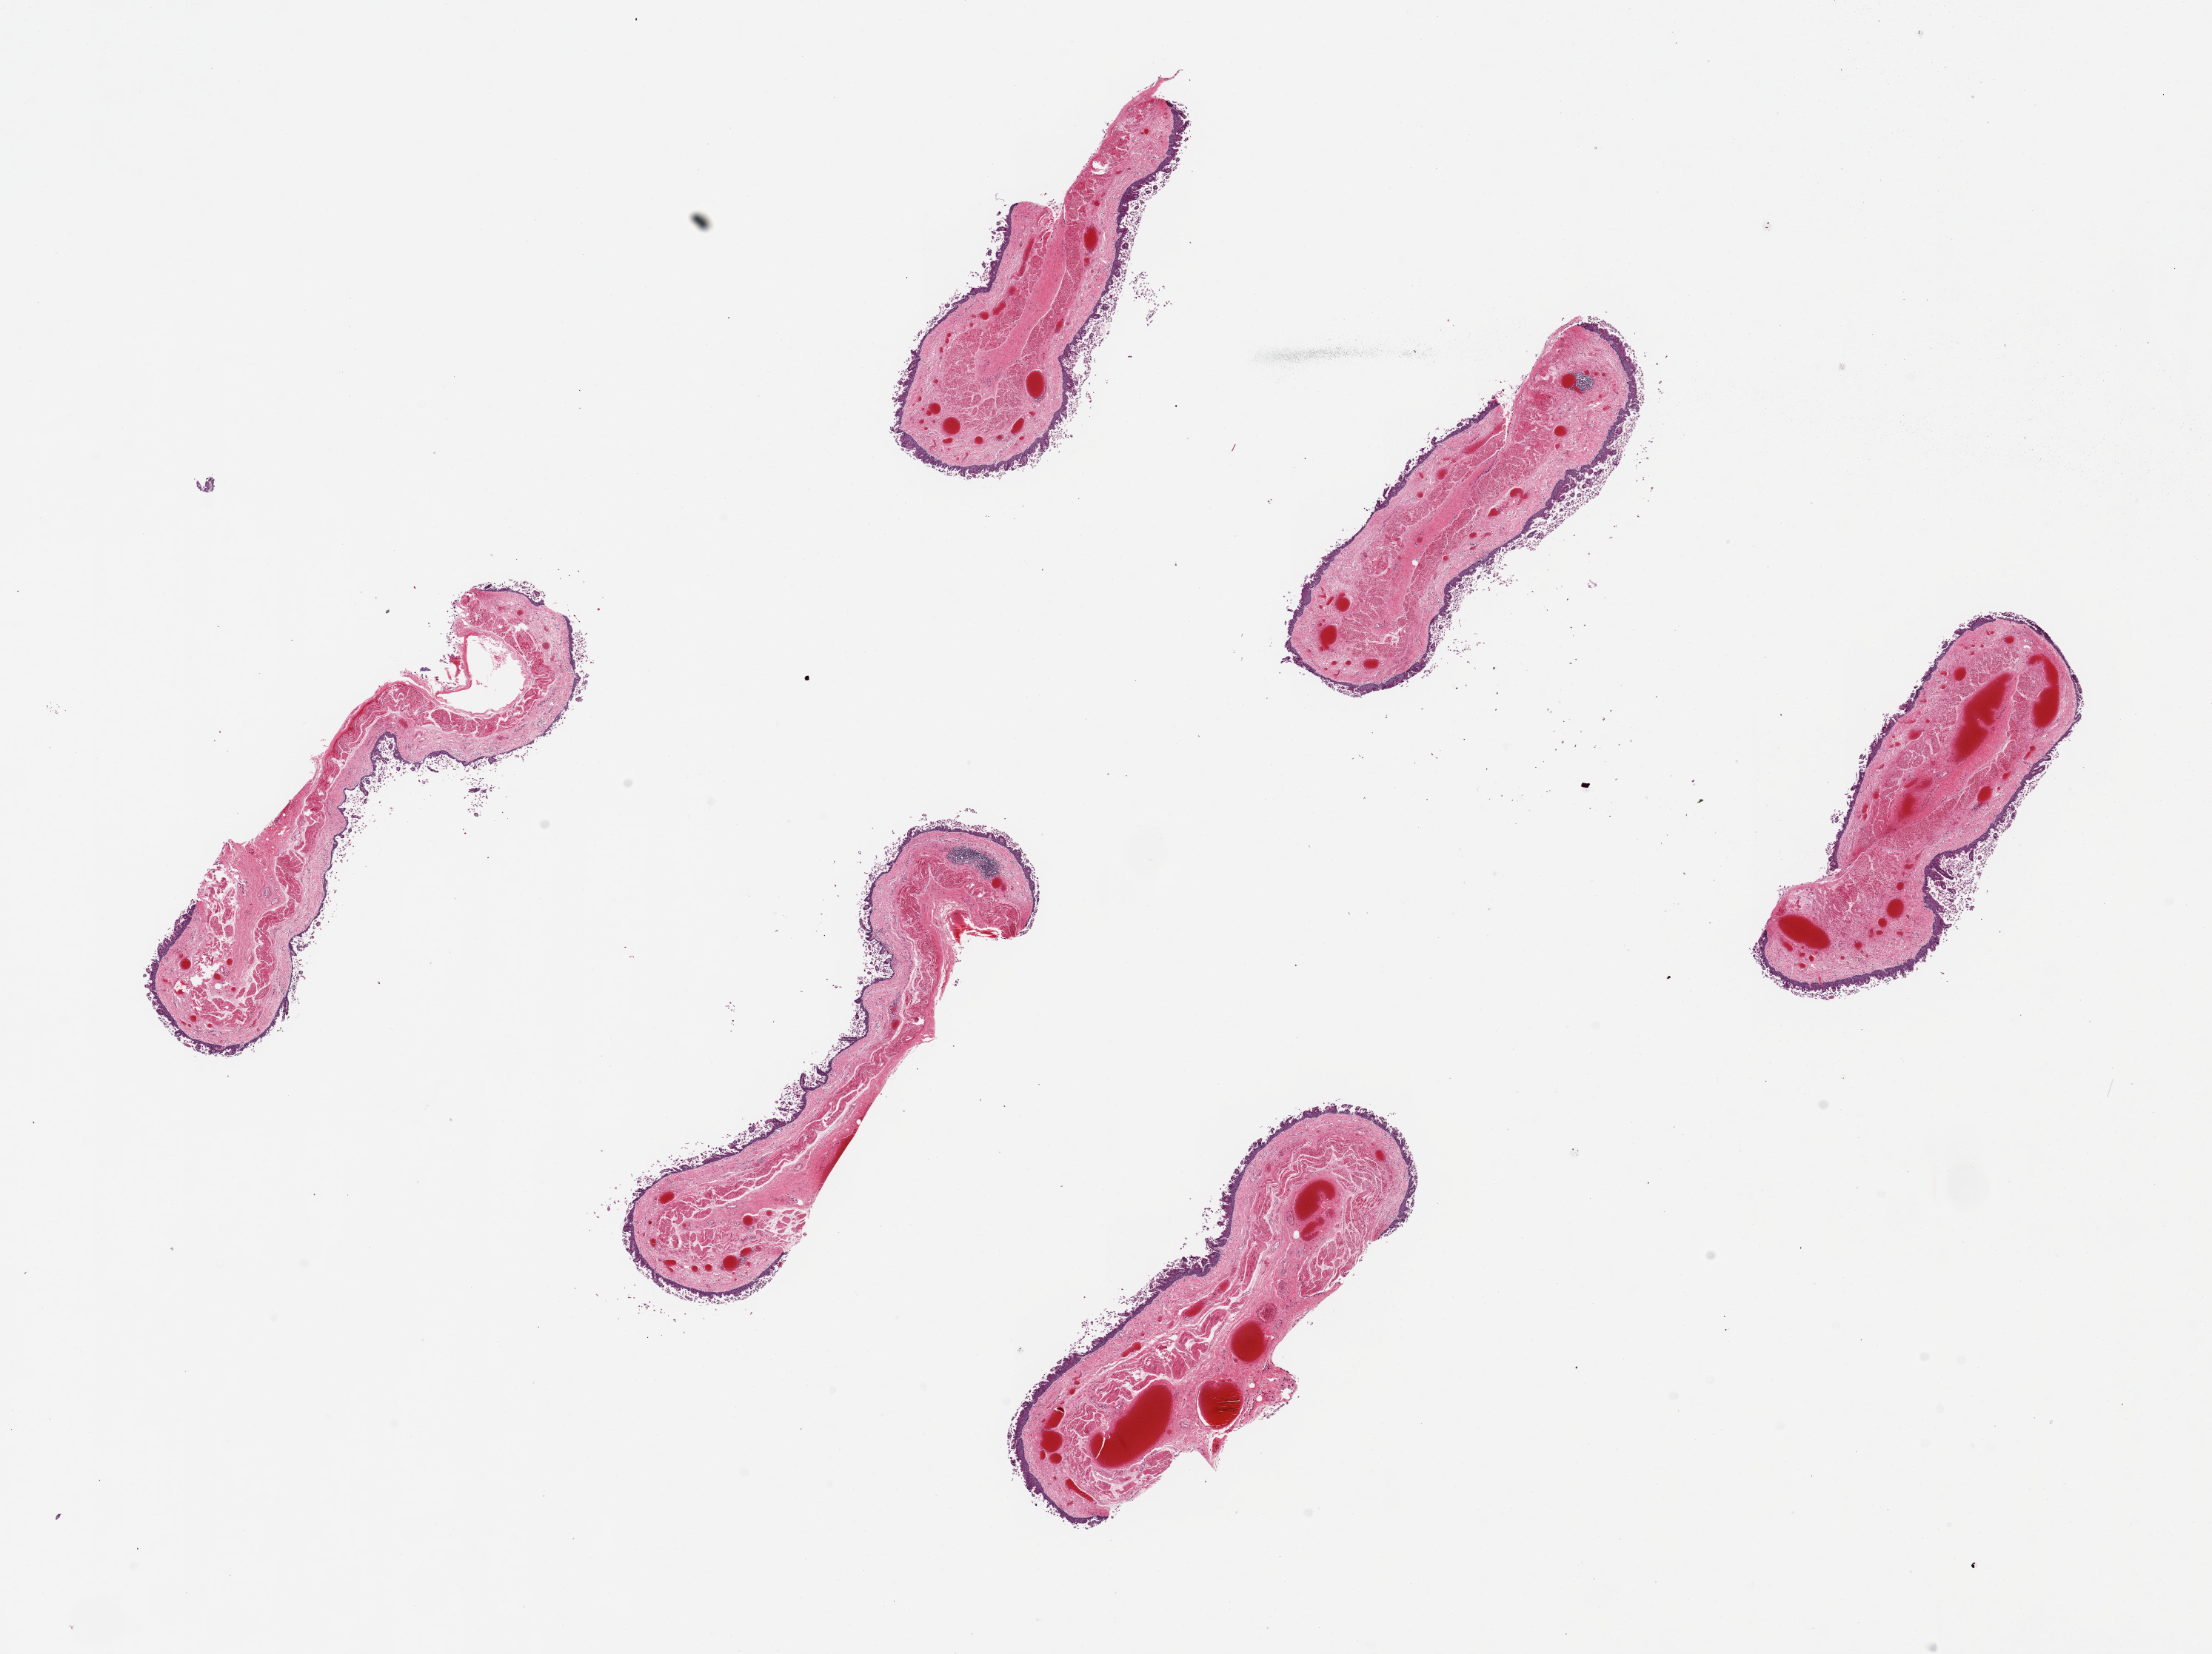
Whole-slide image, H&E stain — shown as a low-resolution overview of the whole scanned area (about 23.6 x 17.7 mm). PAXgene-fixed paraffin-embedded (PFPE) section. Target tissue: esophageal mucous membrane. Tissue donor sample.
• review note (as recorded): 6 pieces, ~6x1.5mm. Squamous mucosa badly autolyzed, partly sloughed, averages ~100 microns thickness